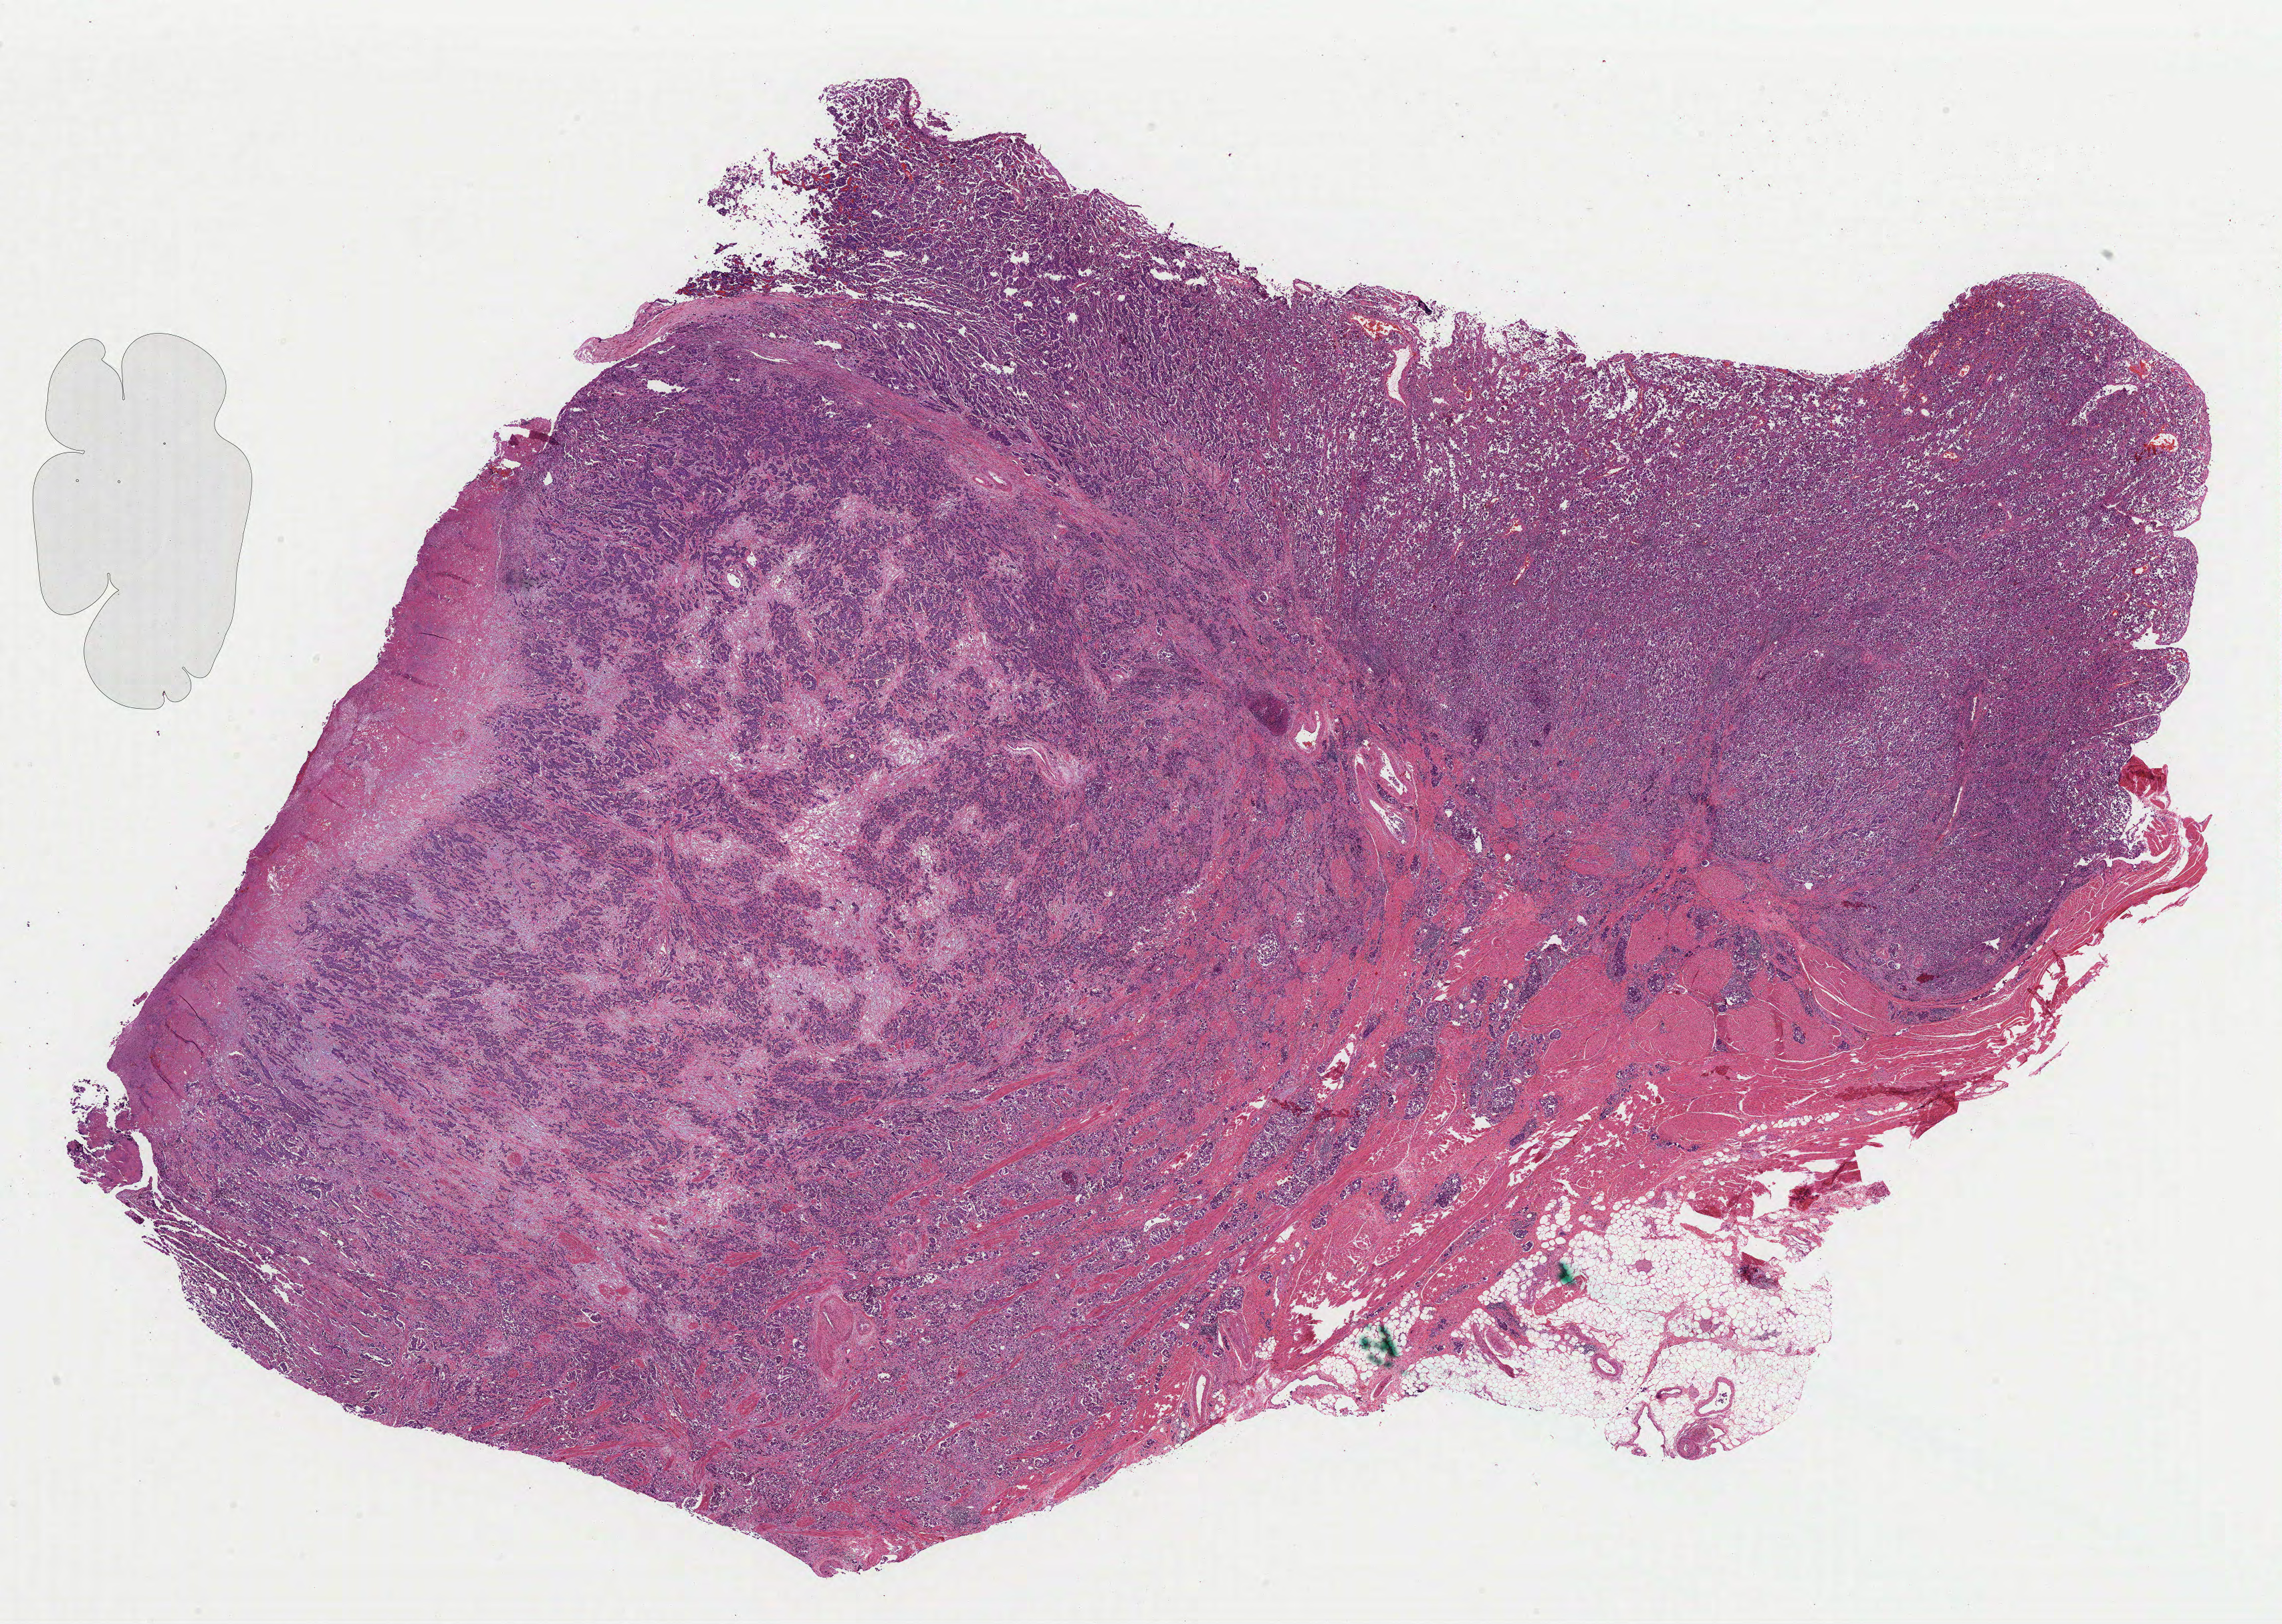
Whole-slide histology image, H&E-stained, shown as a low-resolution overview of the whole scanned area (about 27.1 x 19.3 mm, slide scanned at 40x), FFPE section, primary tumour sample from the bladder. Male, age 55 years at initial diagnosis. Histologic grade: high grade.
TNM: T4a N3 MX. Pathologic diagnosis: Transitional cell carcinoma. Lymph nodes positive (case pathology): 2 of 38 examined. AJCC pathologic stage: IV (7th edition).